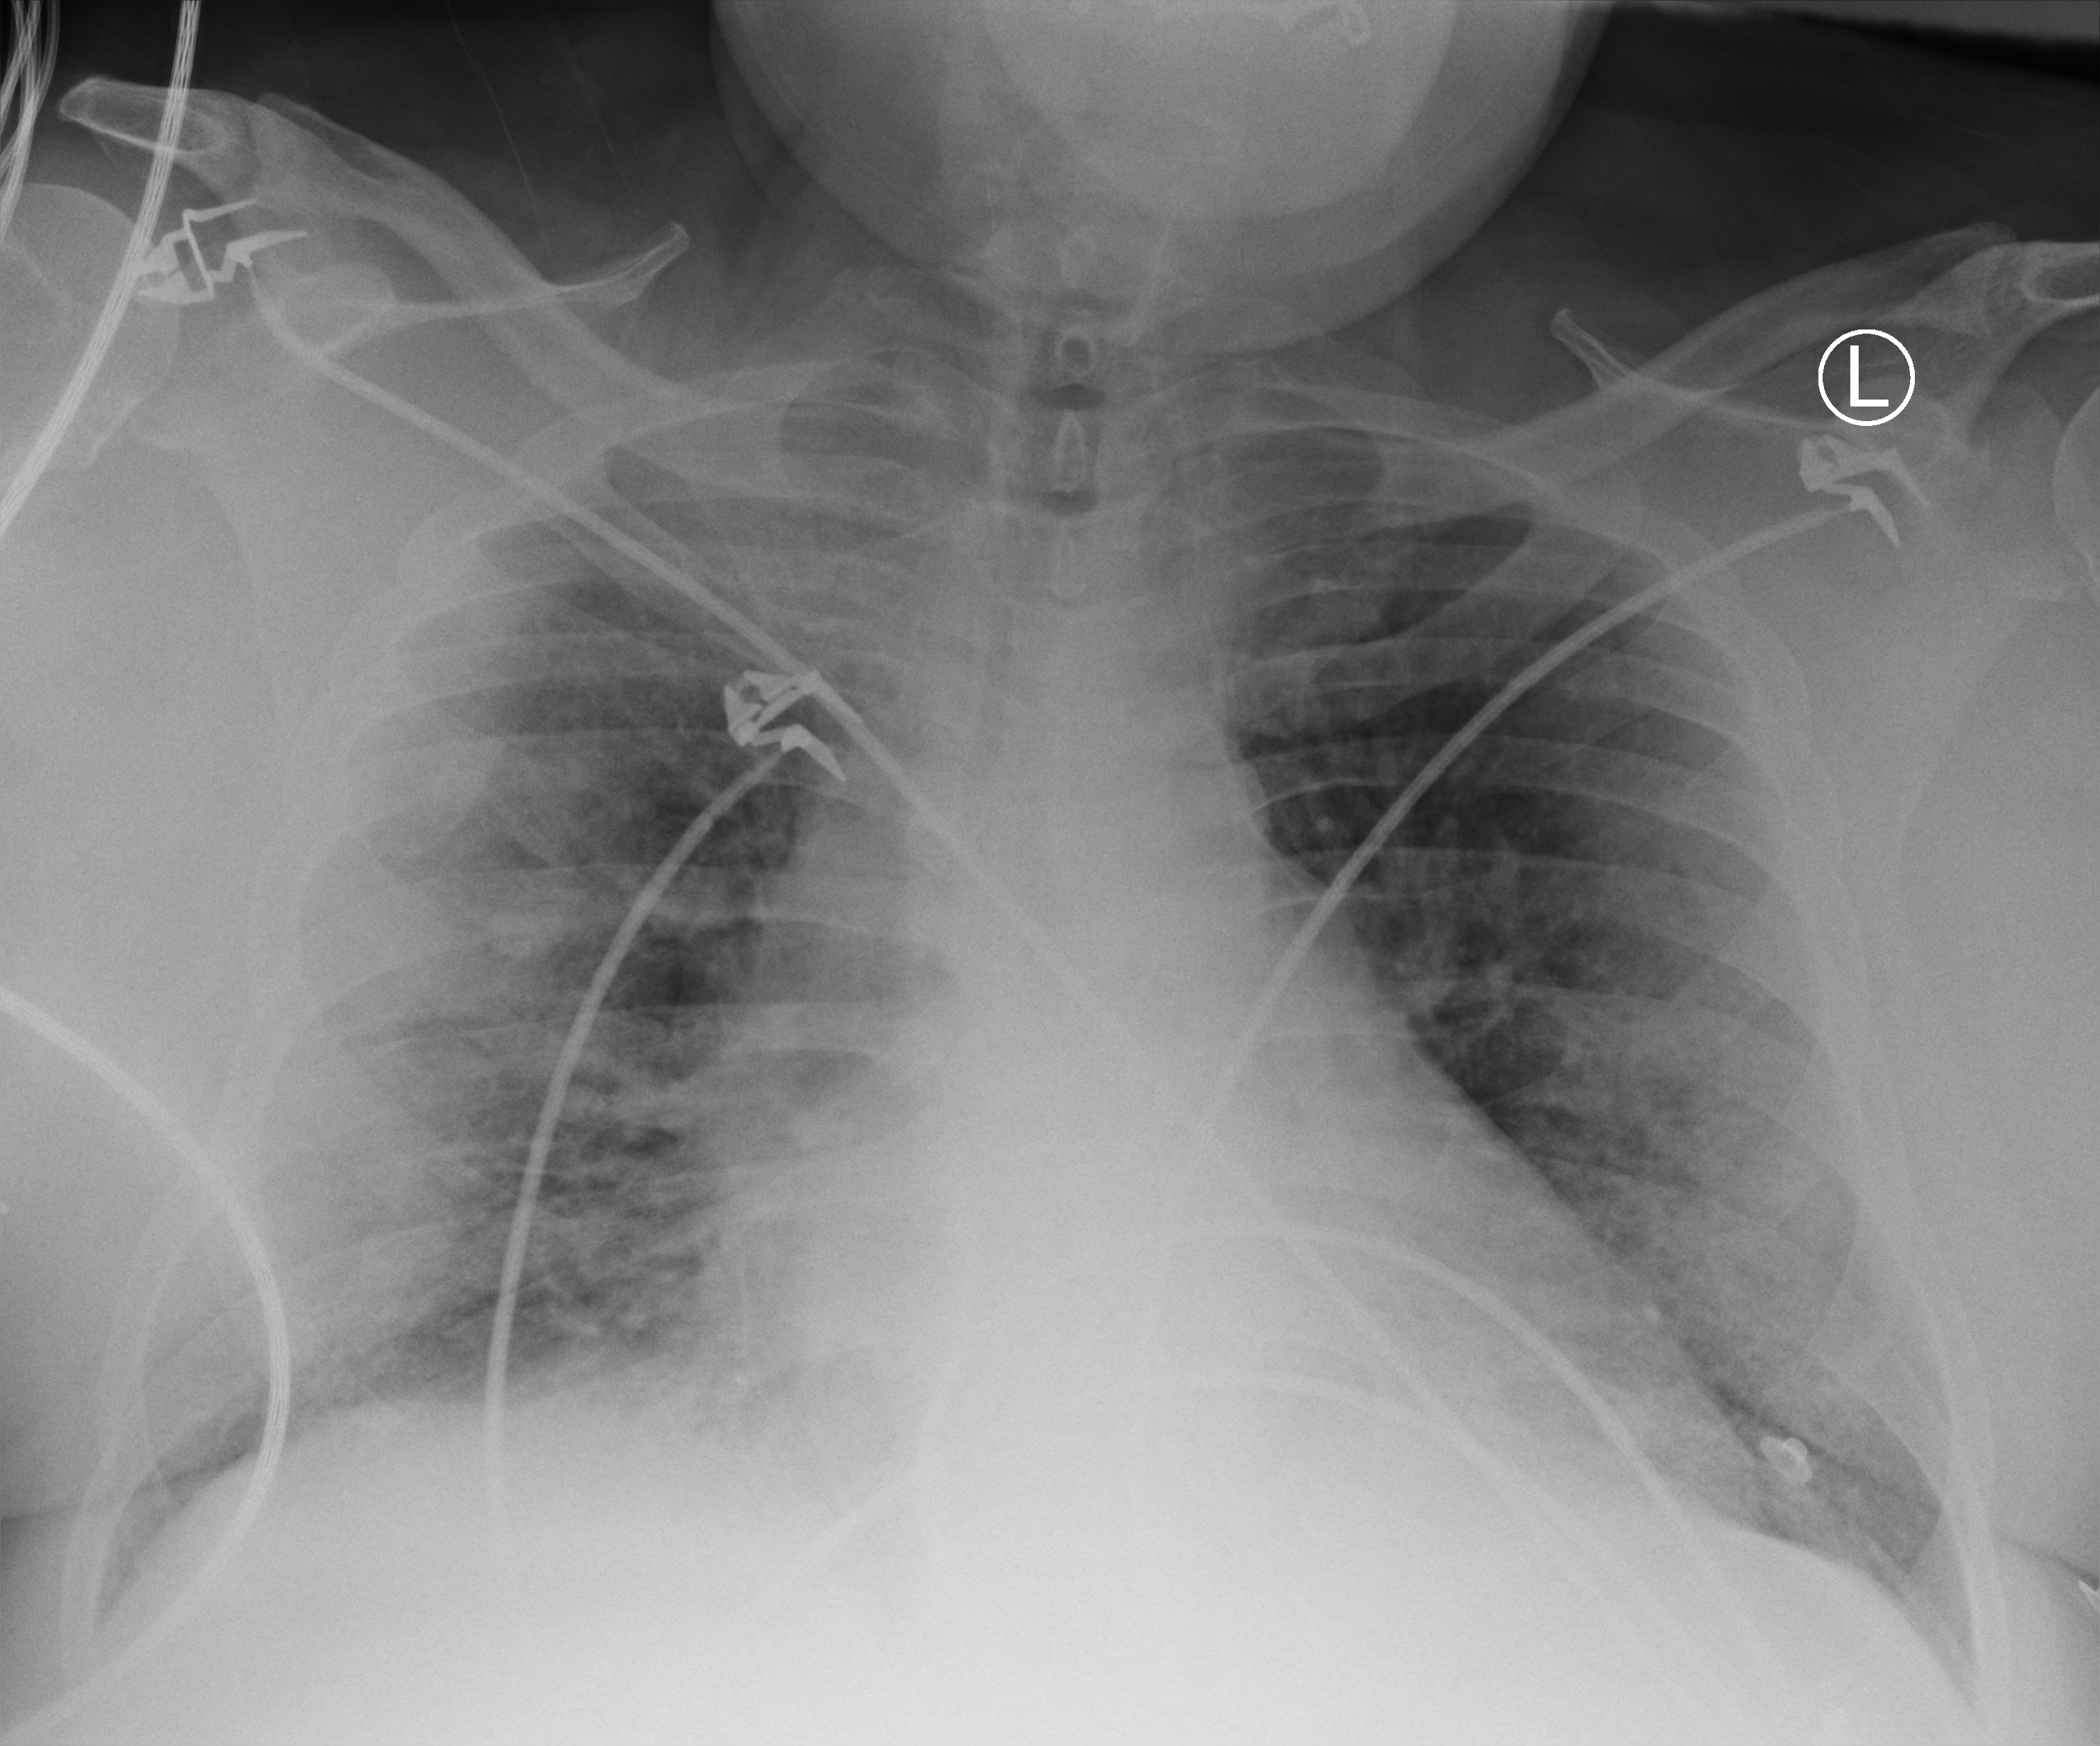
Chest X-ray (portable). Male patient hospitalised with COVID-19, age 60–74 years.
From the hospital-stay record, not from the radiograph (when in the stay this image was taken is not recorded):
- diabetes (admission record): yes
- admitted to intensive care during this hospital stay: yes
- mechanically ventilated during this hospital stay: yes